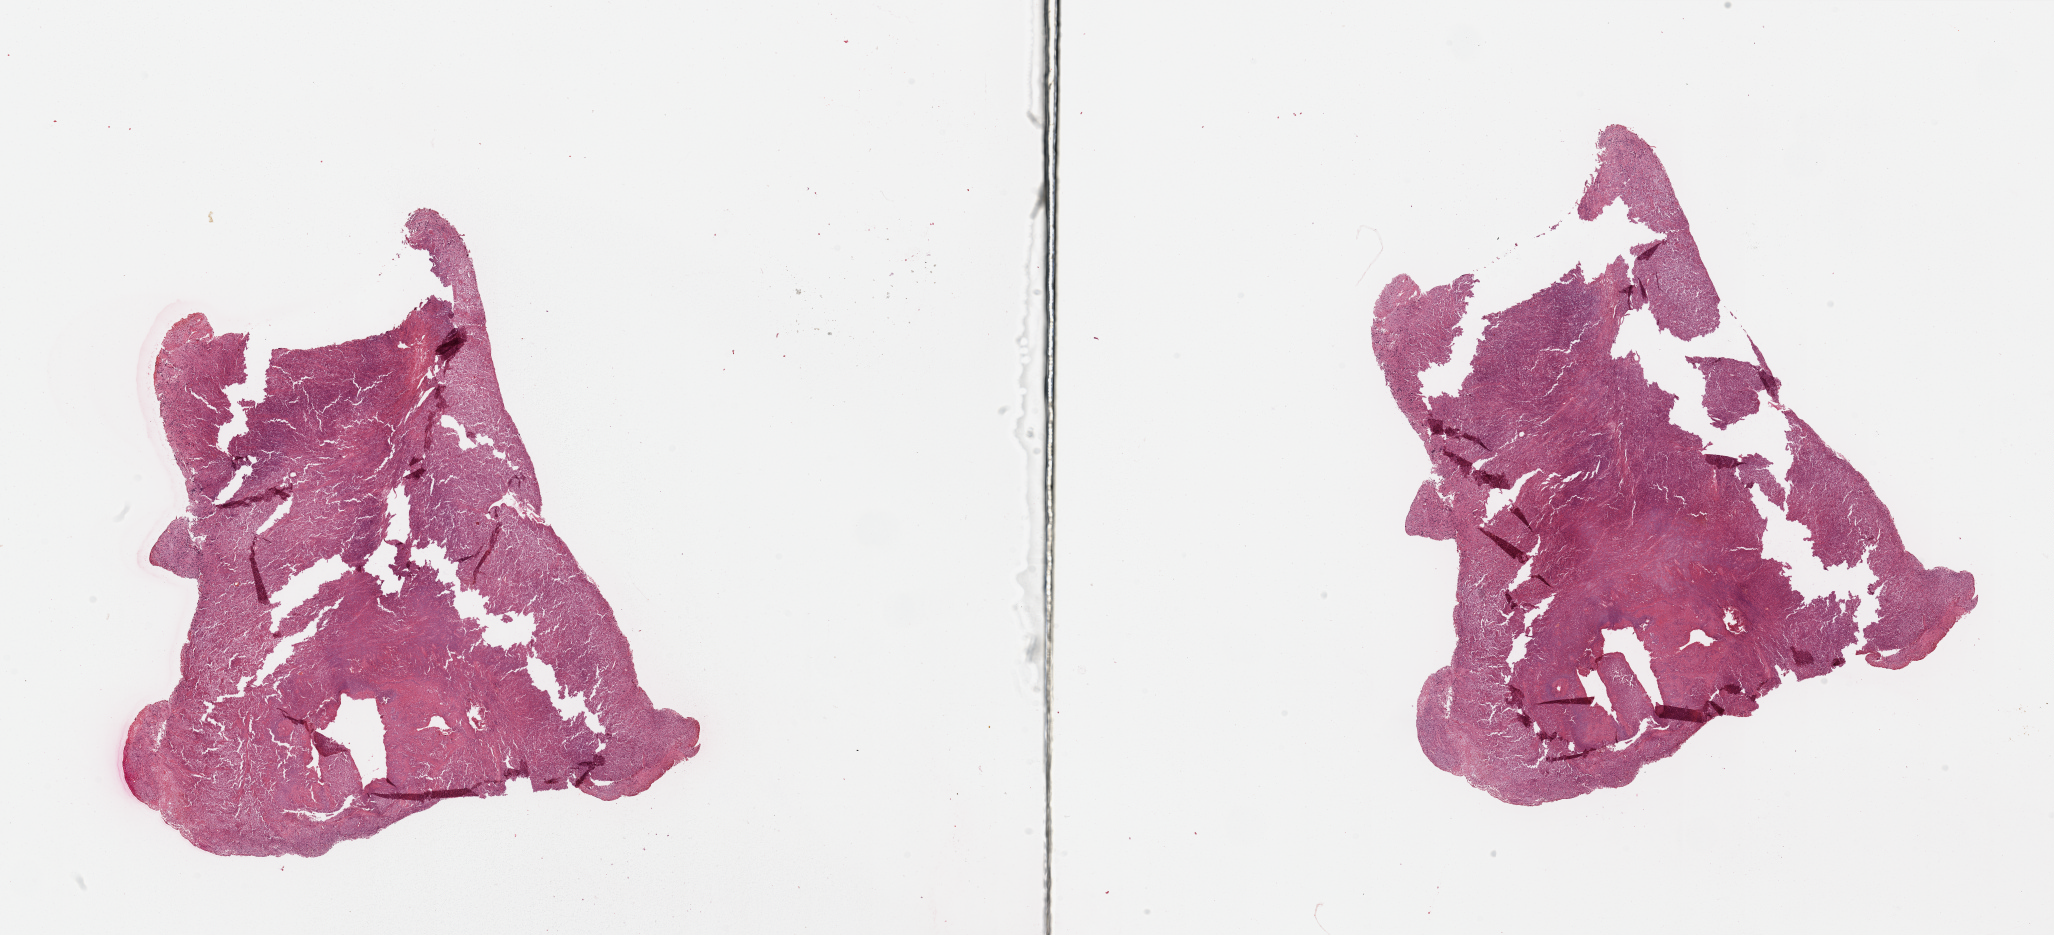
Whole-slide histology image, H&E, shown as a low-resolution overview of the whole scanned area (about 32.5 x 14.8 mm, from a 20x scan). Female, 80 y/o.
• patient diagnosis (cohort enrolment): sarcoma (site not recorded at cohort level)
• primary tumour site (as recorded): gynecologic